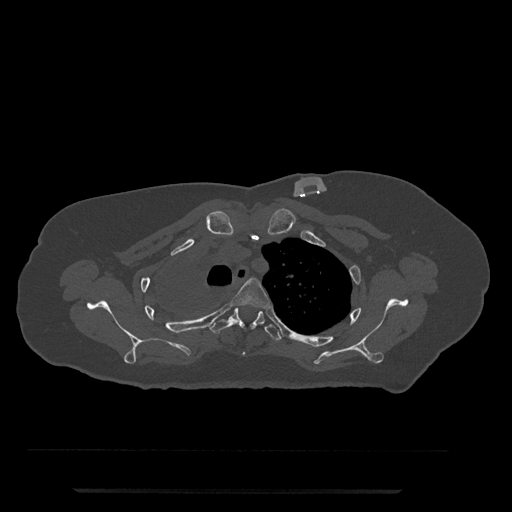
CT including the spine, one axial slice; reconstruction kernel Br40s/3; bone window (W 1800 / L 400 HU); 512 × 512 image matrix, field of view 440 × 440 mm. Female patient, age 51 years. Case-level facts recorded for this patient, not image findings: primary cancer: neuro; vertebrae with lytic lesions (as recorded): T8.
Structures marked on this image (semi-automatically segmented with operator editing):
- T3 vertebra: box from (x=232, y=278) to (x=270, y=355) px
- T4 vertebra: (x=209, y=308)–(x=282, y=341)